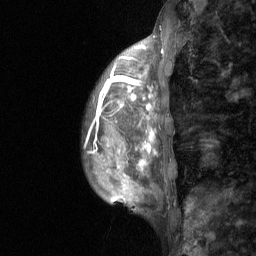
Breast MRI (dynamic contrast-enhanced), one sagittal slice; position 17 of 64 along the scan axis; dynamic contrast-enhanced study with each time point stored as its own series, time point 2 of 3 at this slice position (early post-contrast, ordered by acquisition time); 1.5 T; TE 4.8 ms, TR 27 ms; 2 mm slice thickness; 256 × 256 image matrix. Patient: female, 36 years. Case-level facts recorded for this patient, not image findings: setting: breast cancer imaged before/during neoadjuvant chemotherapy; receptor status: HR-positive, HER2-negative.
Annotated regions visible in this slice (semi-automatically segmented with operator editing):
- analysis volume of interest (the breast-tissue region the enhancement analysis was run in; not a lesion): bounding box (x1, y1, x2, y2) in pixels: (84, 102, 176, 210)
- tumour enhancement mask (voxels above the 90 % enhancement threshold inside the analysis volume of interest): (95, 102, 150, 164)